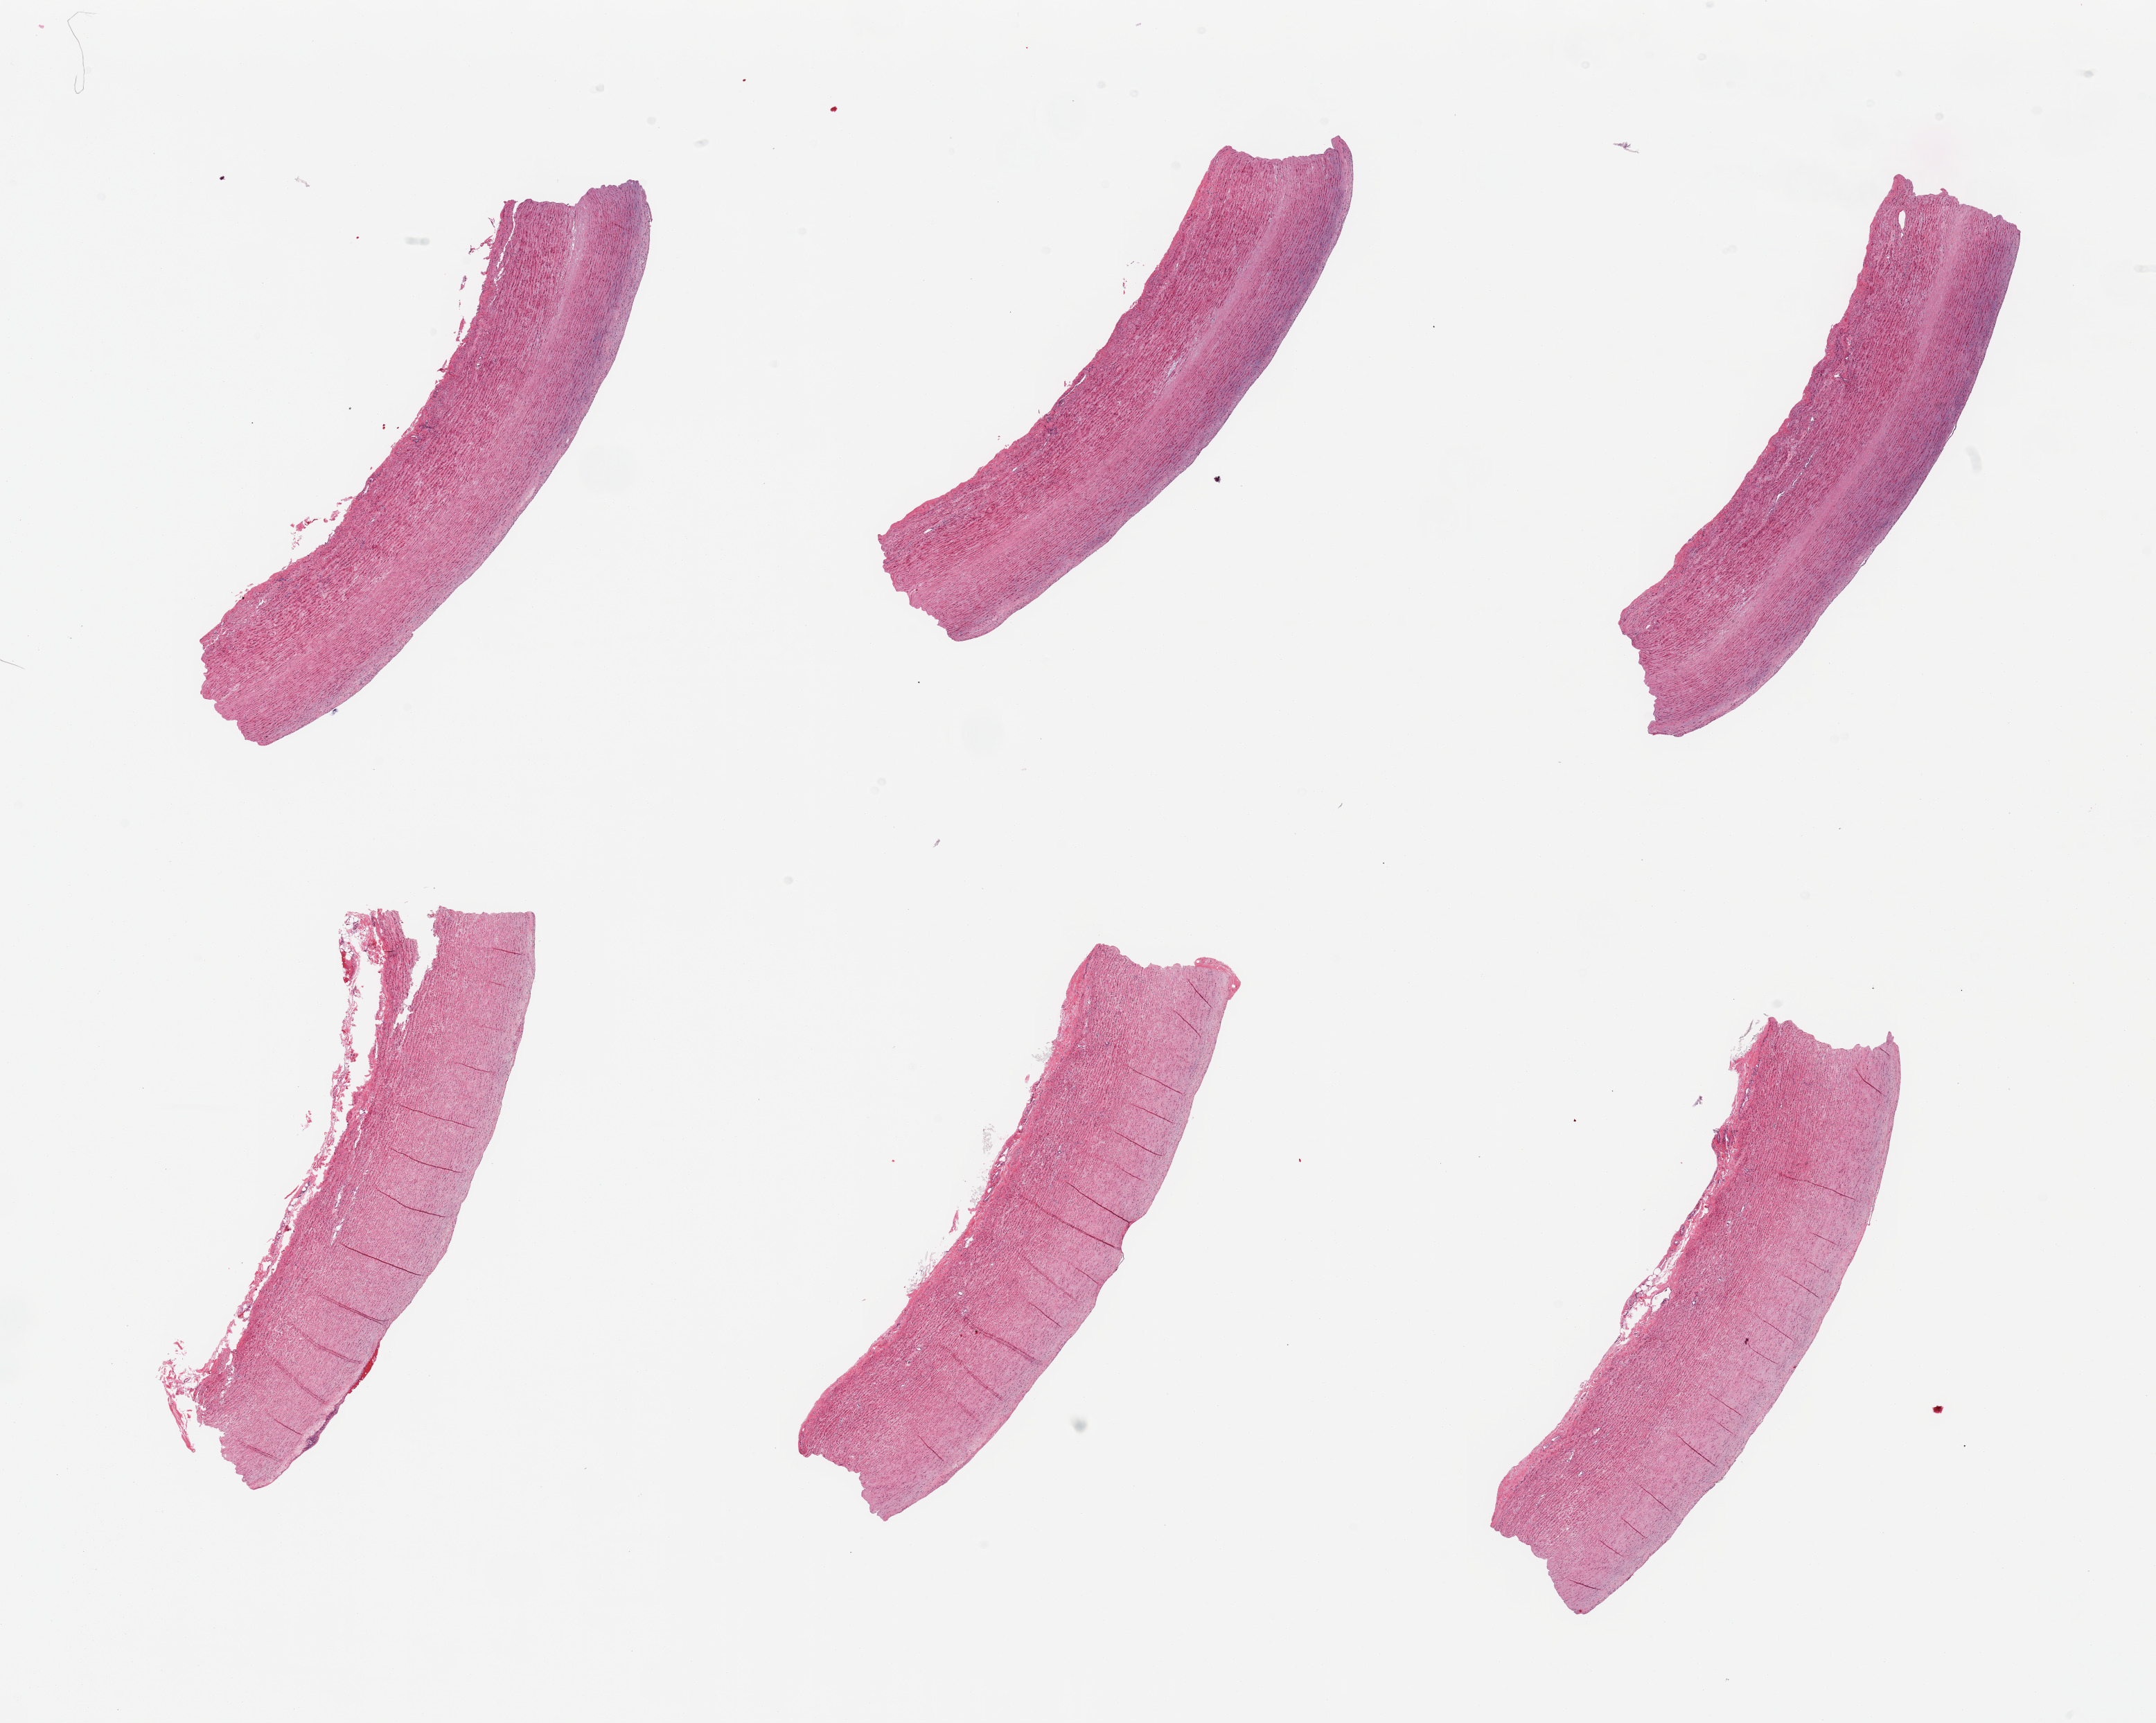
Whole-slide image, haematoxylin and eosin stain — shown as a low-resolution overview of the whole scanned area (about 24.6 x 19.7 mm, slide scanned at 20x), PAXgene-fixed paraffin-embedded (PFPE) section, sampled site (target tissue): aorta, donor tissue sample. Donor sex: male.
Pathologist's review note for this sample: 6 pieces; intimal edema.